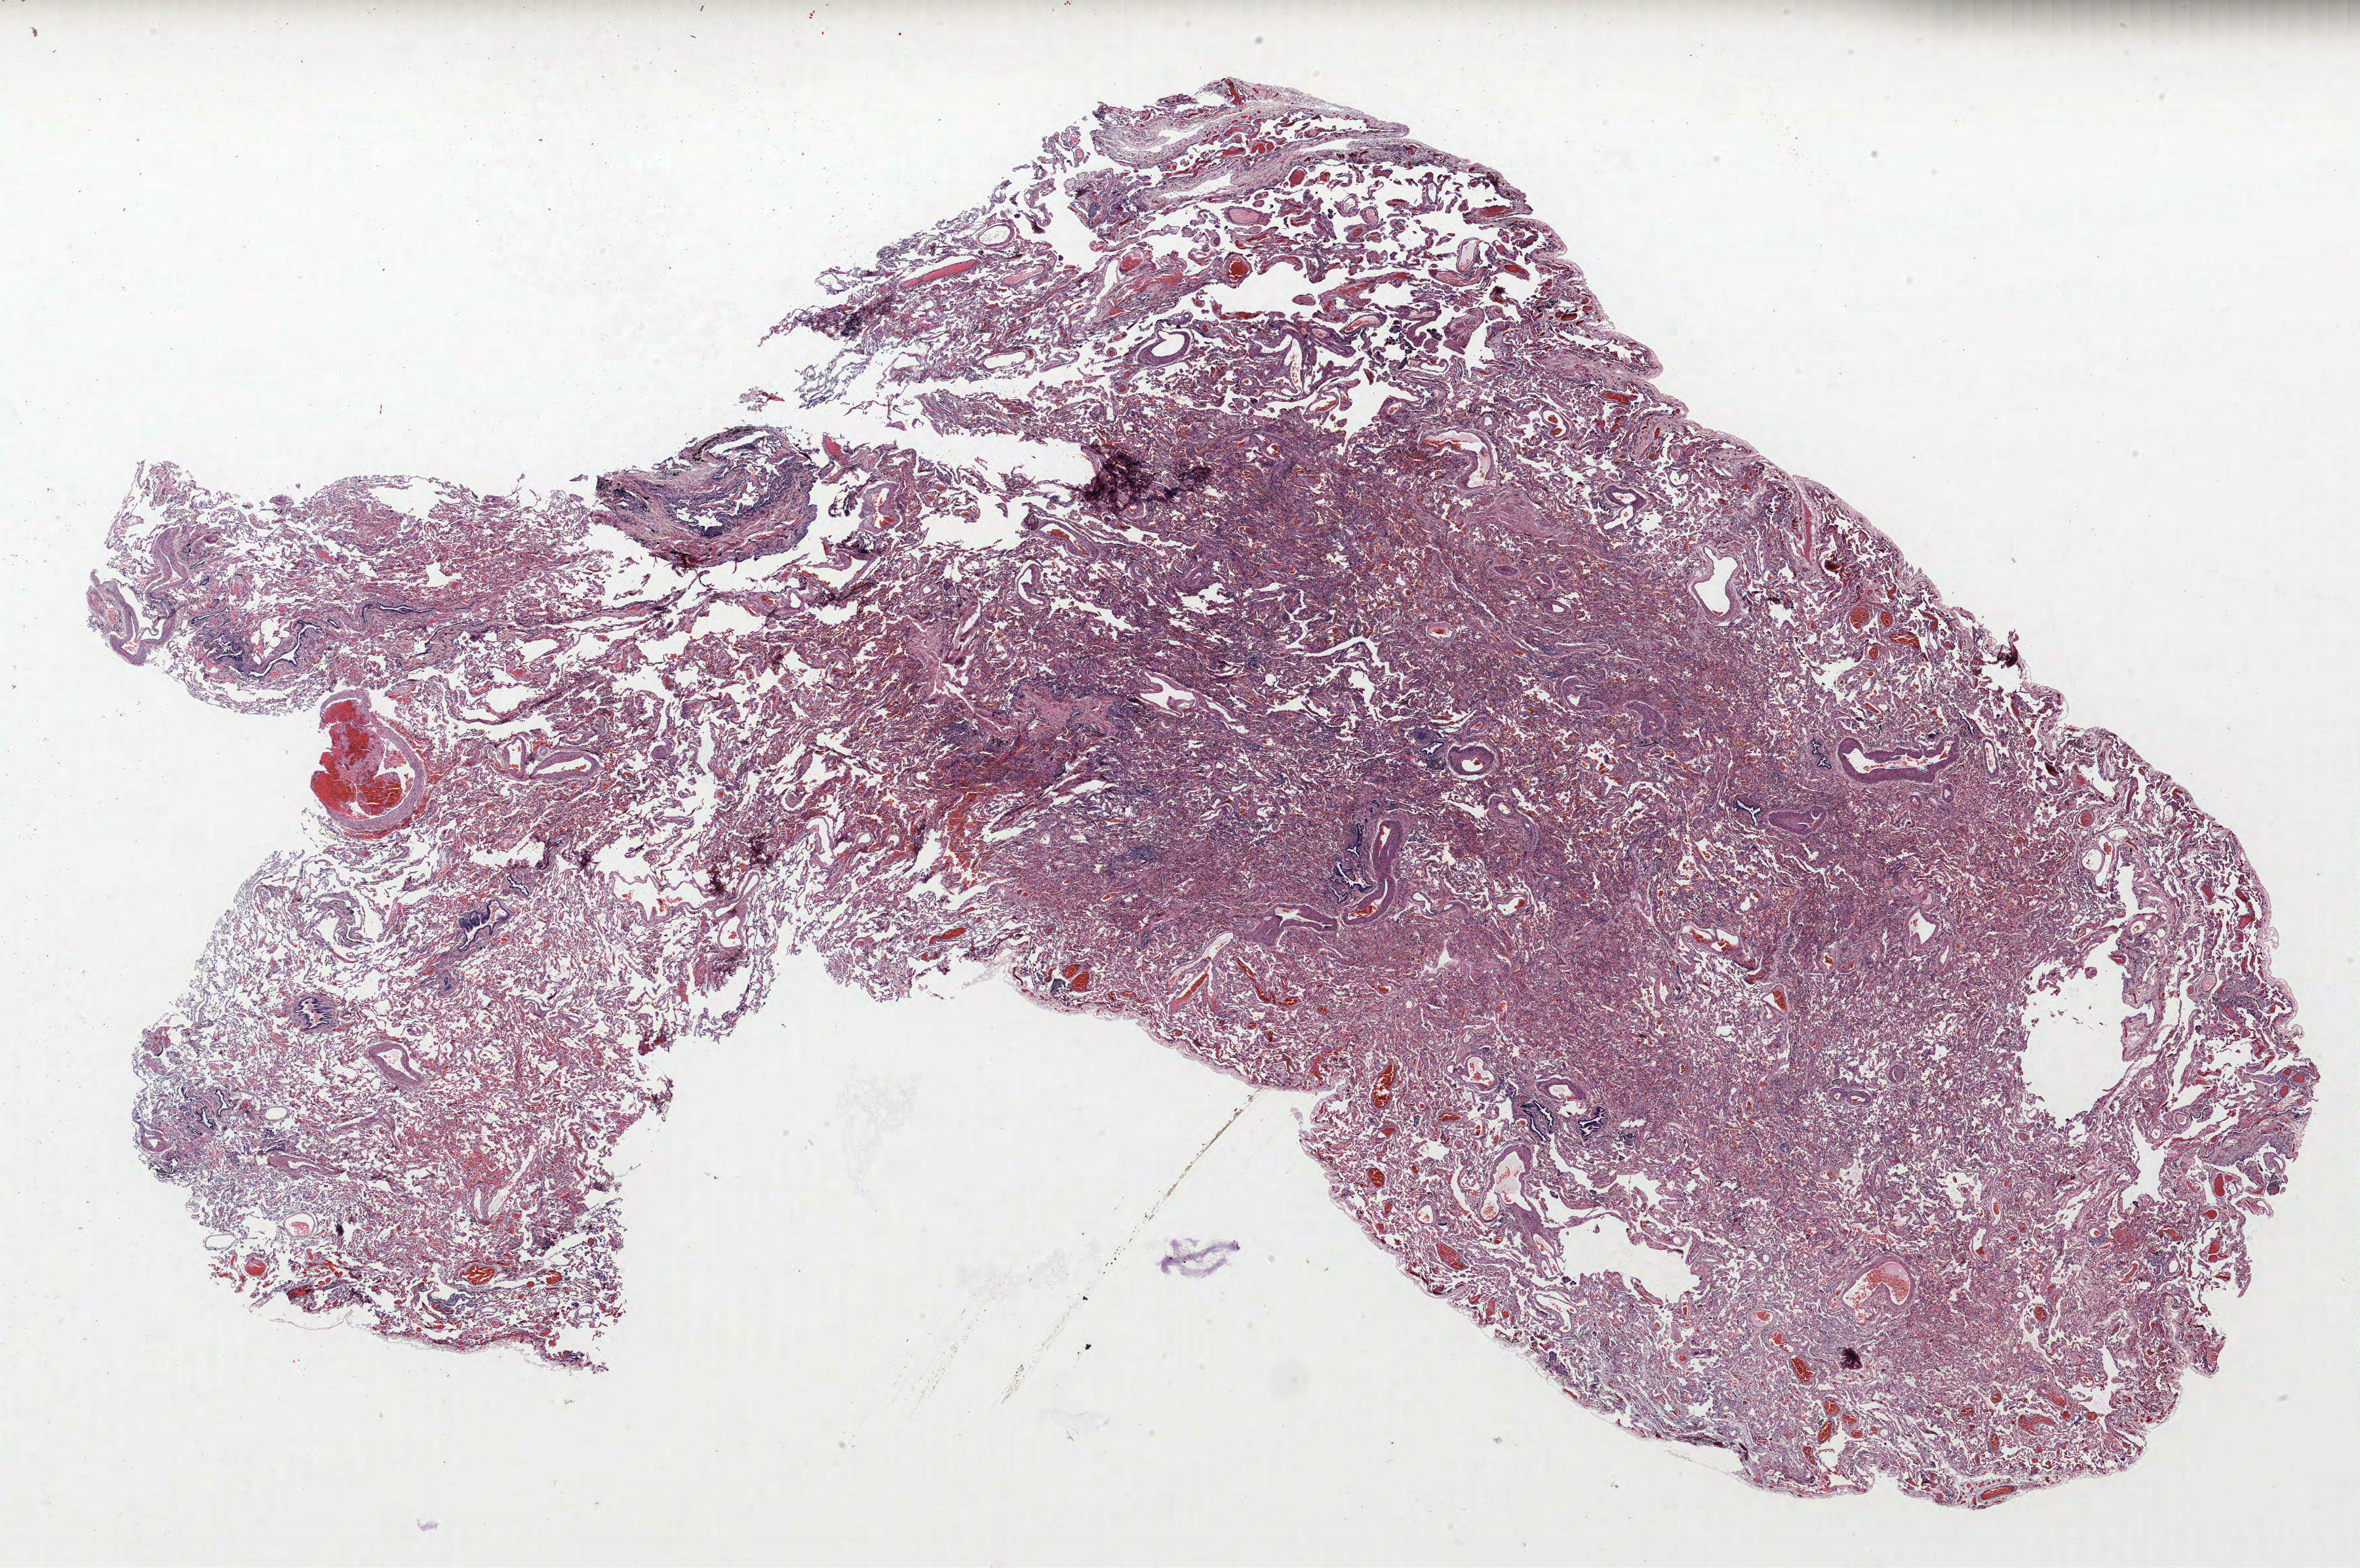
H&E whole-slide image — whole scanned area (about 28.8 x 19.1 mm, slide scanned at 40x) shown as a low-resolution overview; formalin-fixed paraffin-embedded (FFPE) section; lung tissue. Female, age 63 at enrolment. Former smoker at enrolment. Grade: well differentiated (G1).
Primary tumour location (clinical record): right upper lobe. Stage (AJCC 6th edition): IA. Participant's lung-cancer diagnosis: Bronchiolo-alveolar carcinoma, non-mucinous. Tumour size (pathology): 12 mm.